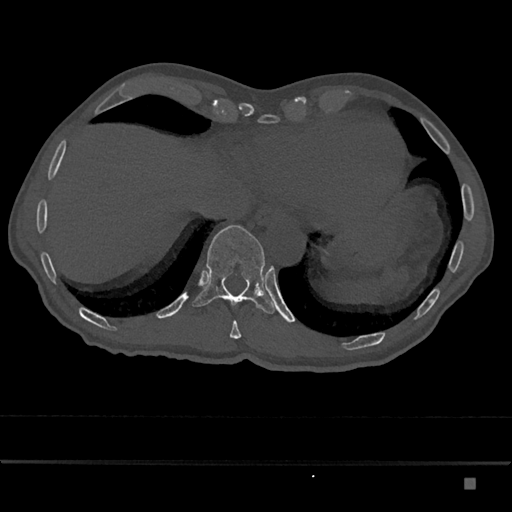
CT including the spine, one axial slice; slice 693 of 797 in the series (ordered by position); reconstruction kernel Br40s/3; bone window (W 1800 / L 400 HU); 512 × 512 image matrix, field of view 390 × 390 mm. Male patient, age 72 years. Case-level facts recorded for this patient, not image findings: primary cancer: prostate.
Outlined on this slice (semi-automatically segmented with operator editing):
- T10 vertebra: bounding box [x1, y1, x2, y2] px = [230, 321, 242, 339]
- T11 vertebra: [192, 225, 275, 314]